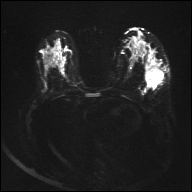
Breast MRI, one axial slice. Position 18 of 32 along the scan axis. Diffusion-weighted series; image 2 of 4 stored at this slice position (different b-values; order by instance number). 1.5 T. 4 mm slice thickness. 192 × 192 image matrix, field of view 360 × 360 mm. Female patient.
Outlined on this slice (expert manual segmentation):
- tumour on diffusion-weighted imaging: box from (x=147, y=67) to (x=160, y=81) px